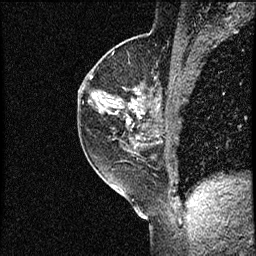
Breast MRI (dynamic contrast-enhanced), one sagittal slice; slice 37 of 56 in the series (ordered by position); dynamic contrast-enhanced study with each time point stored as its own series, time point 2 of 3 at this slice position (early post-contrast, ordered by acquisition time); 1.5 T; TE 4.2 ms, TR 17.3 ms; 2 mm slice thickness; 256 × 256 image matrix, field of view 200 × 200 mm. Female patient. Case-level facts recorded for this patient, not image findings: setting: breast cancer imaged before/during neoadjuvant chemotherapy; receptor status: HER2-positive.
Outlined on this slice (semi-automatic segmentation, software-assisted and operator-edited):
- analysis volume of interest (the breast-tissue region the enhancement analysis was run in; not a lesion): bounding box <77,50,156,155> (left, top, right, bottom; pixels)
- tumour enhancement mask (voxels above the 100 % enhancement threshold inside the analysis volume of interest): <91,93,144,124>